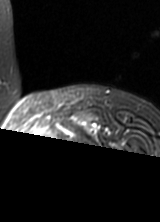
MRI of an extremity soft-tissue mass, one axial slice. Slice 56 of 69 in the series (ordered by position). T2-weighted fat-saturated. MR volume resampled by the dataset authors to the PET/CT grid (not the native acquisition matrix). 160 × 222 image matrix, field of view 156 × 217 mm. Female patient. From the clinical record (not read from this slice): histological type: pleomorphic leiomyosarcoma; grade: high; site of the primary tumour: left thigh.
Structures marked on this image (expert contour drawn on MRI and transferred to this co-registered scan by the dataset authors):
- gross tumour volume including surrounding oedema: box from (x=32, y=130) to (x=55, y=151) px